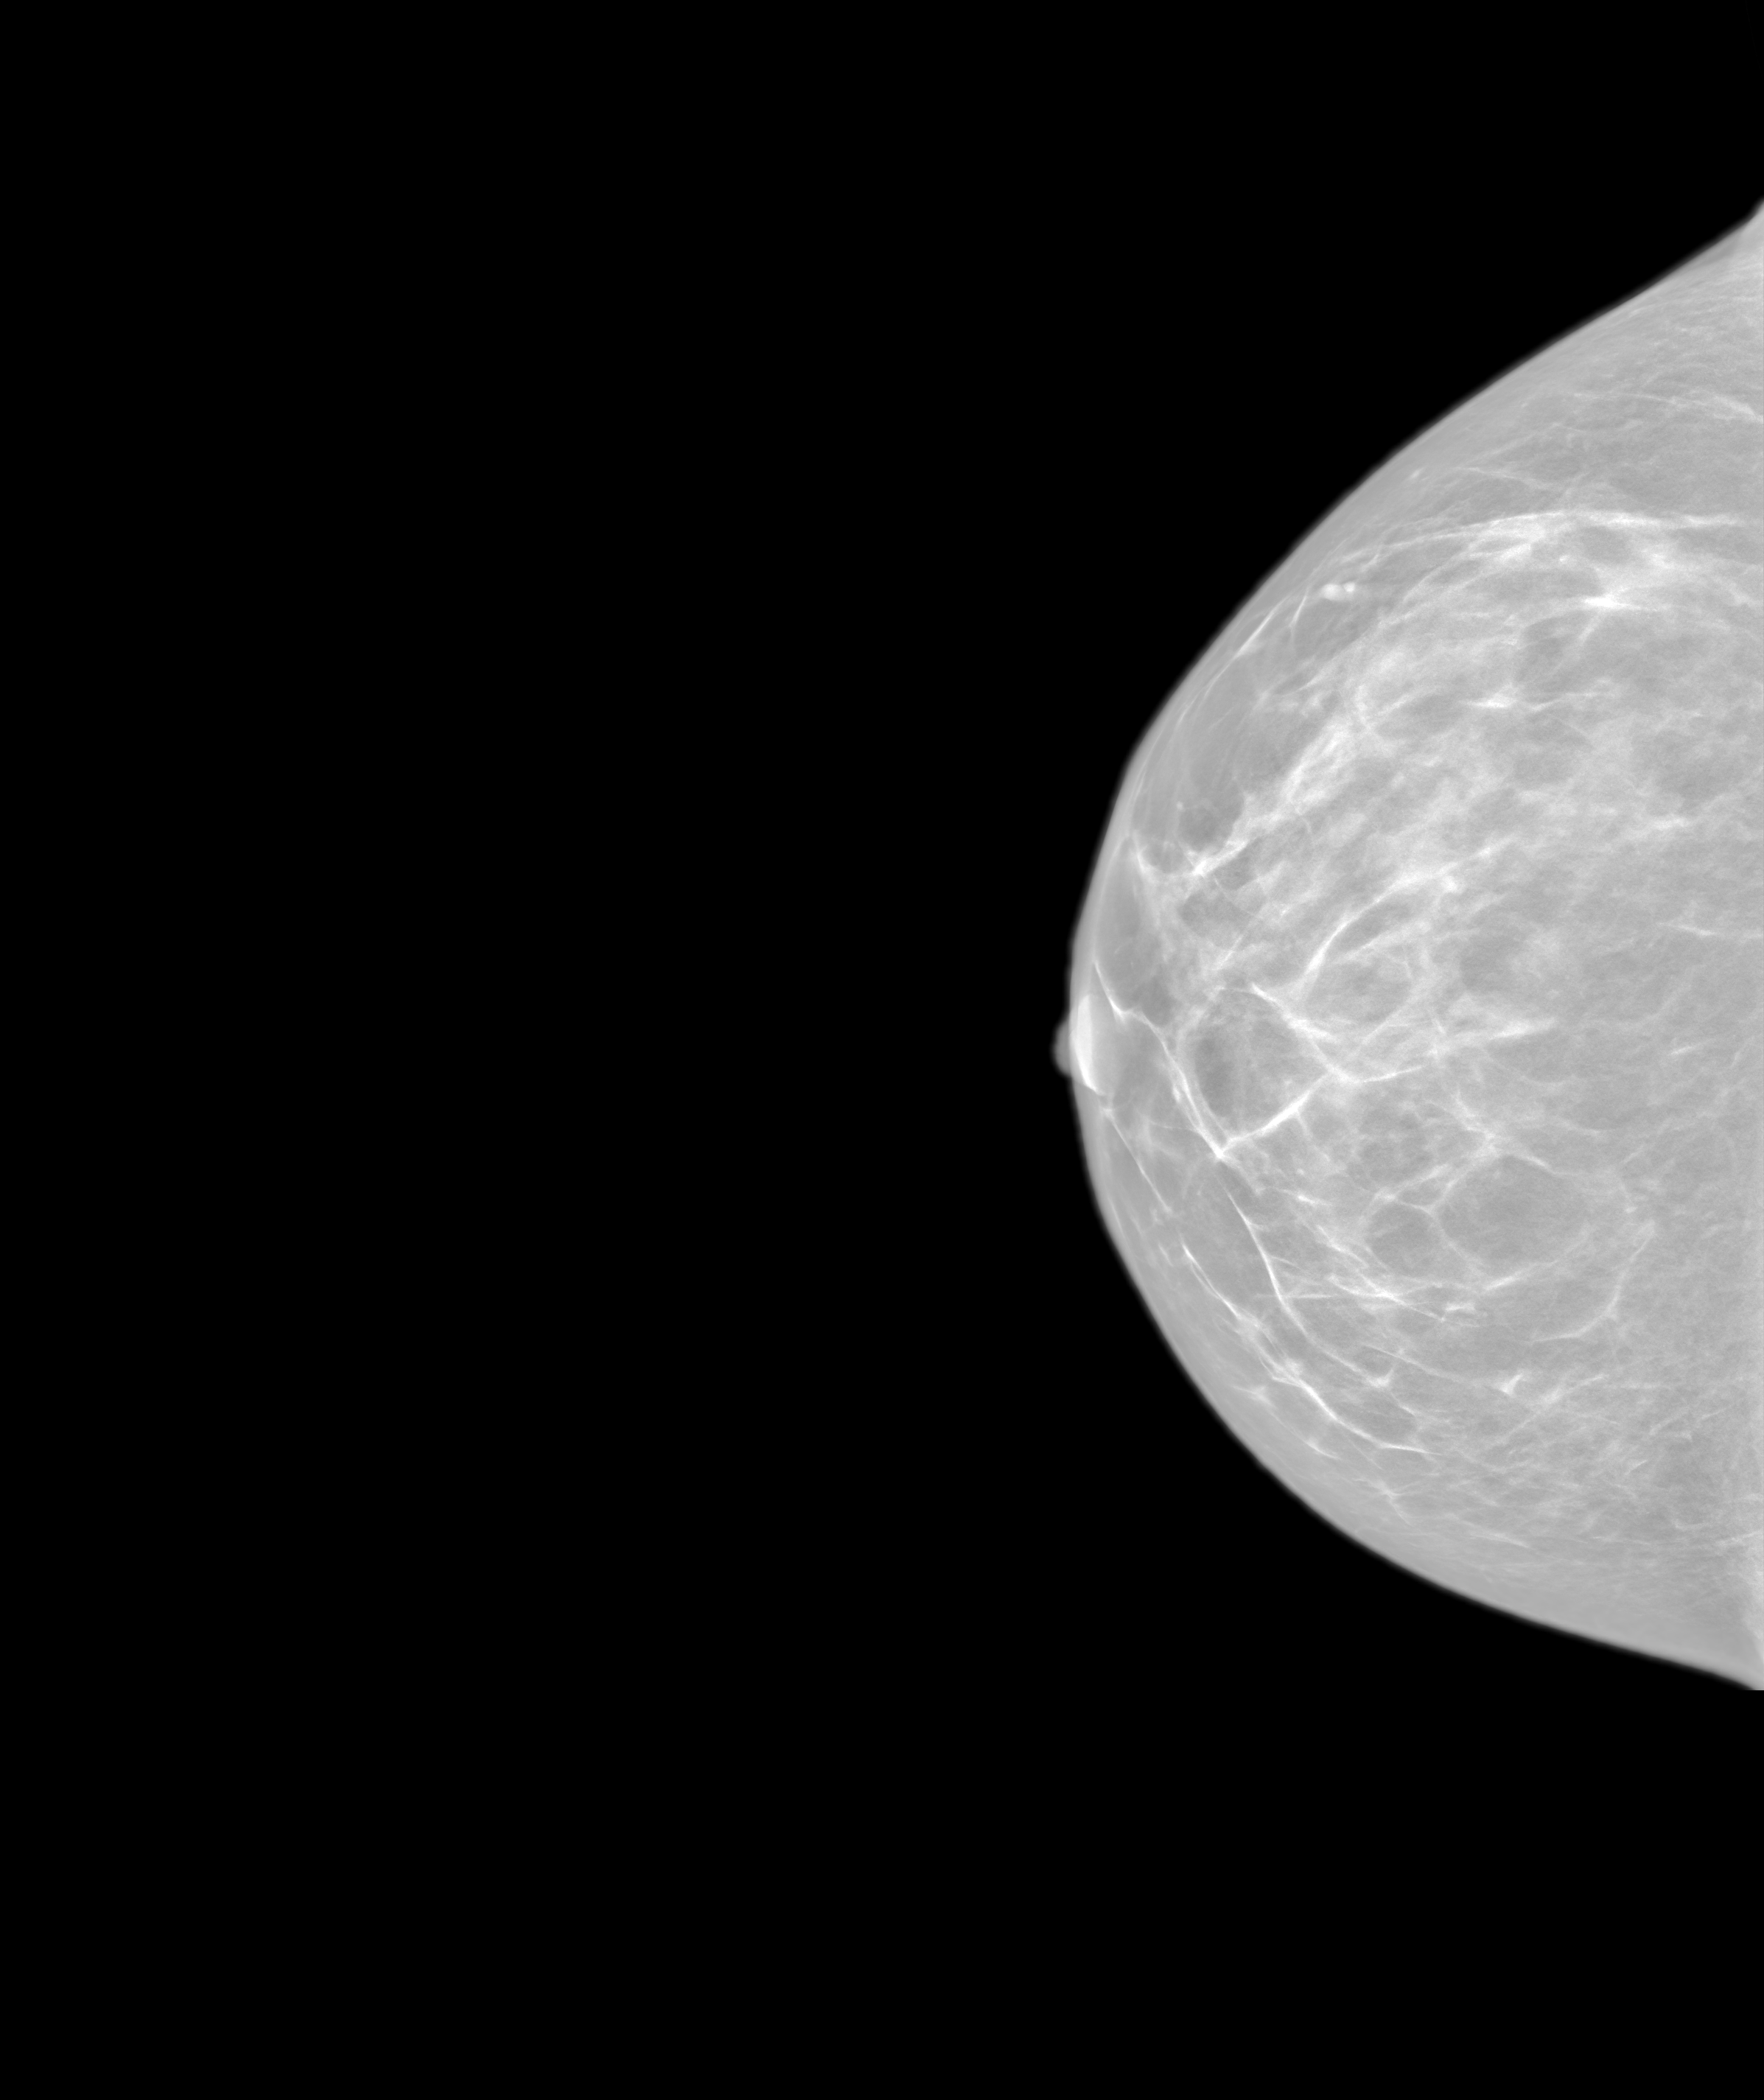
Annual screening mammography examination; system: SenoIris_1SP2(440). Female patient, age 46 years.
Image type: synthesized 2-D view from tomosynthesis. Breast: right. Projection: craniocaudal (CC) view.